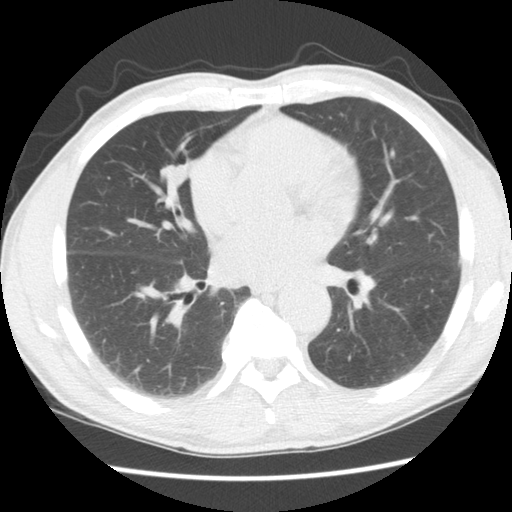
Axial slice from a low-dose chest CT screening exam, second screening round (one year after baseline), lung window (W 1500 / L -600 HU), 2.5 mm slice thickness, slice 81 of 152 in the series. Male, age 65 years at enrolment.
Lesion marked by an expert reader, bounding box (x1, y1, x2, y2) in pixels: (133, 151, 198, 211). The exam's reader record, not a measurement of the box and not confirmed to be the same lesion: non-calcified nodule or mass ≥4 mm, right middle lobe, 11 × 9 mm, smooth margins, soft tissue attenuation, pre-existing on the prior screen: no. Official screen result: positive, other. Later outcome: lung cancer diagnosed 601 days after this screen — squamous cell carcinoma, NOS, right middle lobe, poorly differentiated (G3), stage IA (AJCC 6th edition), 23 mm at pathology.